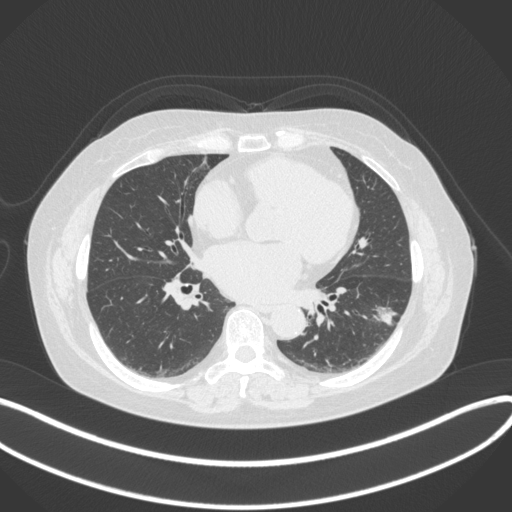
Chest CT, one axial slice. Reconstruction kernel B31f. Lung window (W 1500 / L -600 HU). 1 mm slice thickness. 512 × 512 image matrix, field of view 400 × 400 mm. Patient: female, 67 years. From the clinical record (not read from this slice): clinical TNM (as recorded): T1c N0 M0; histopathological grade: G2.
Annotated regions visible in this slice (bounding box drawn by a radiologist):
- lung tumour (recorded histology: adenocarcinoma): bounding box [x1, y1, x2, y2] px = [370, 300, 403, 332]